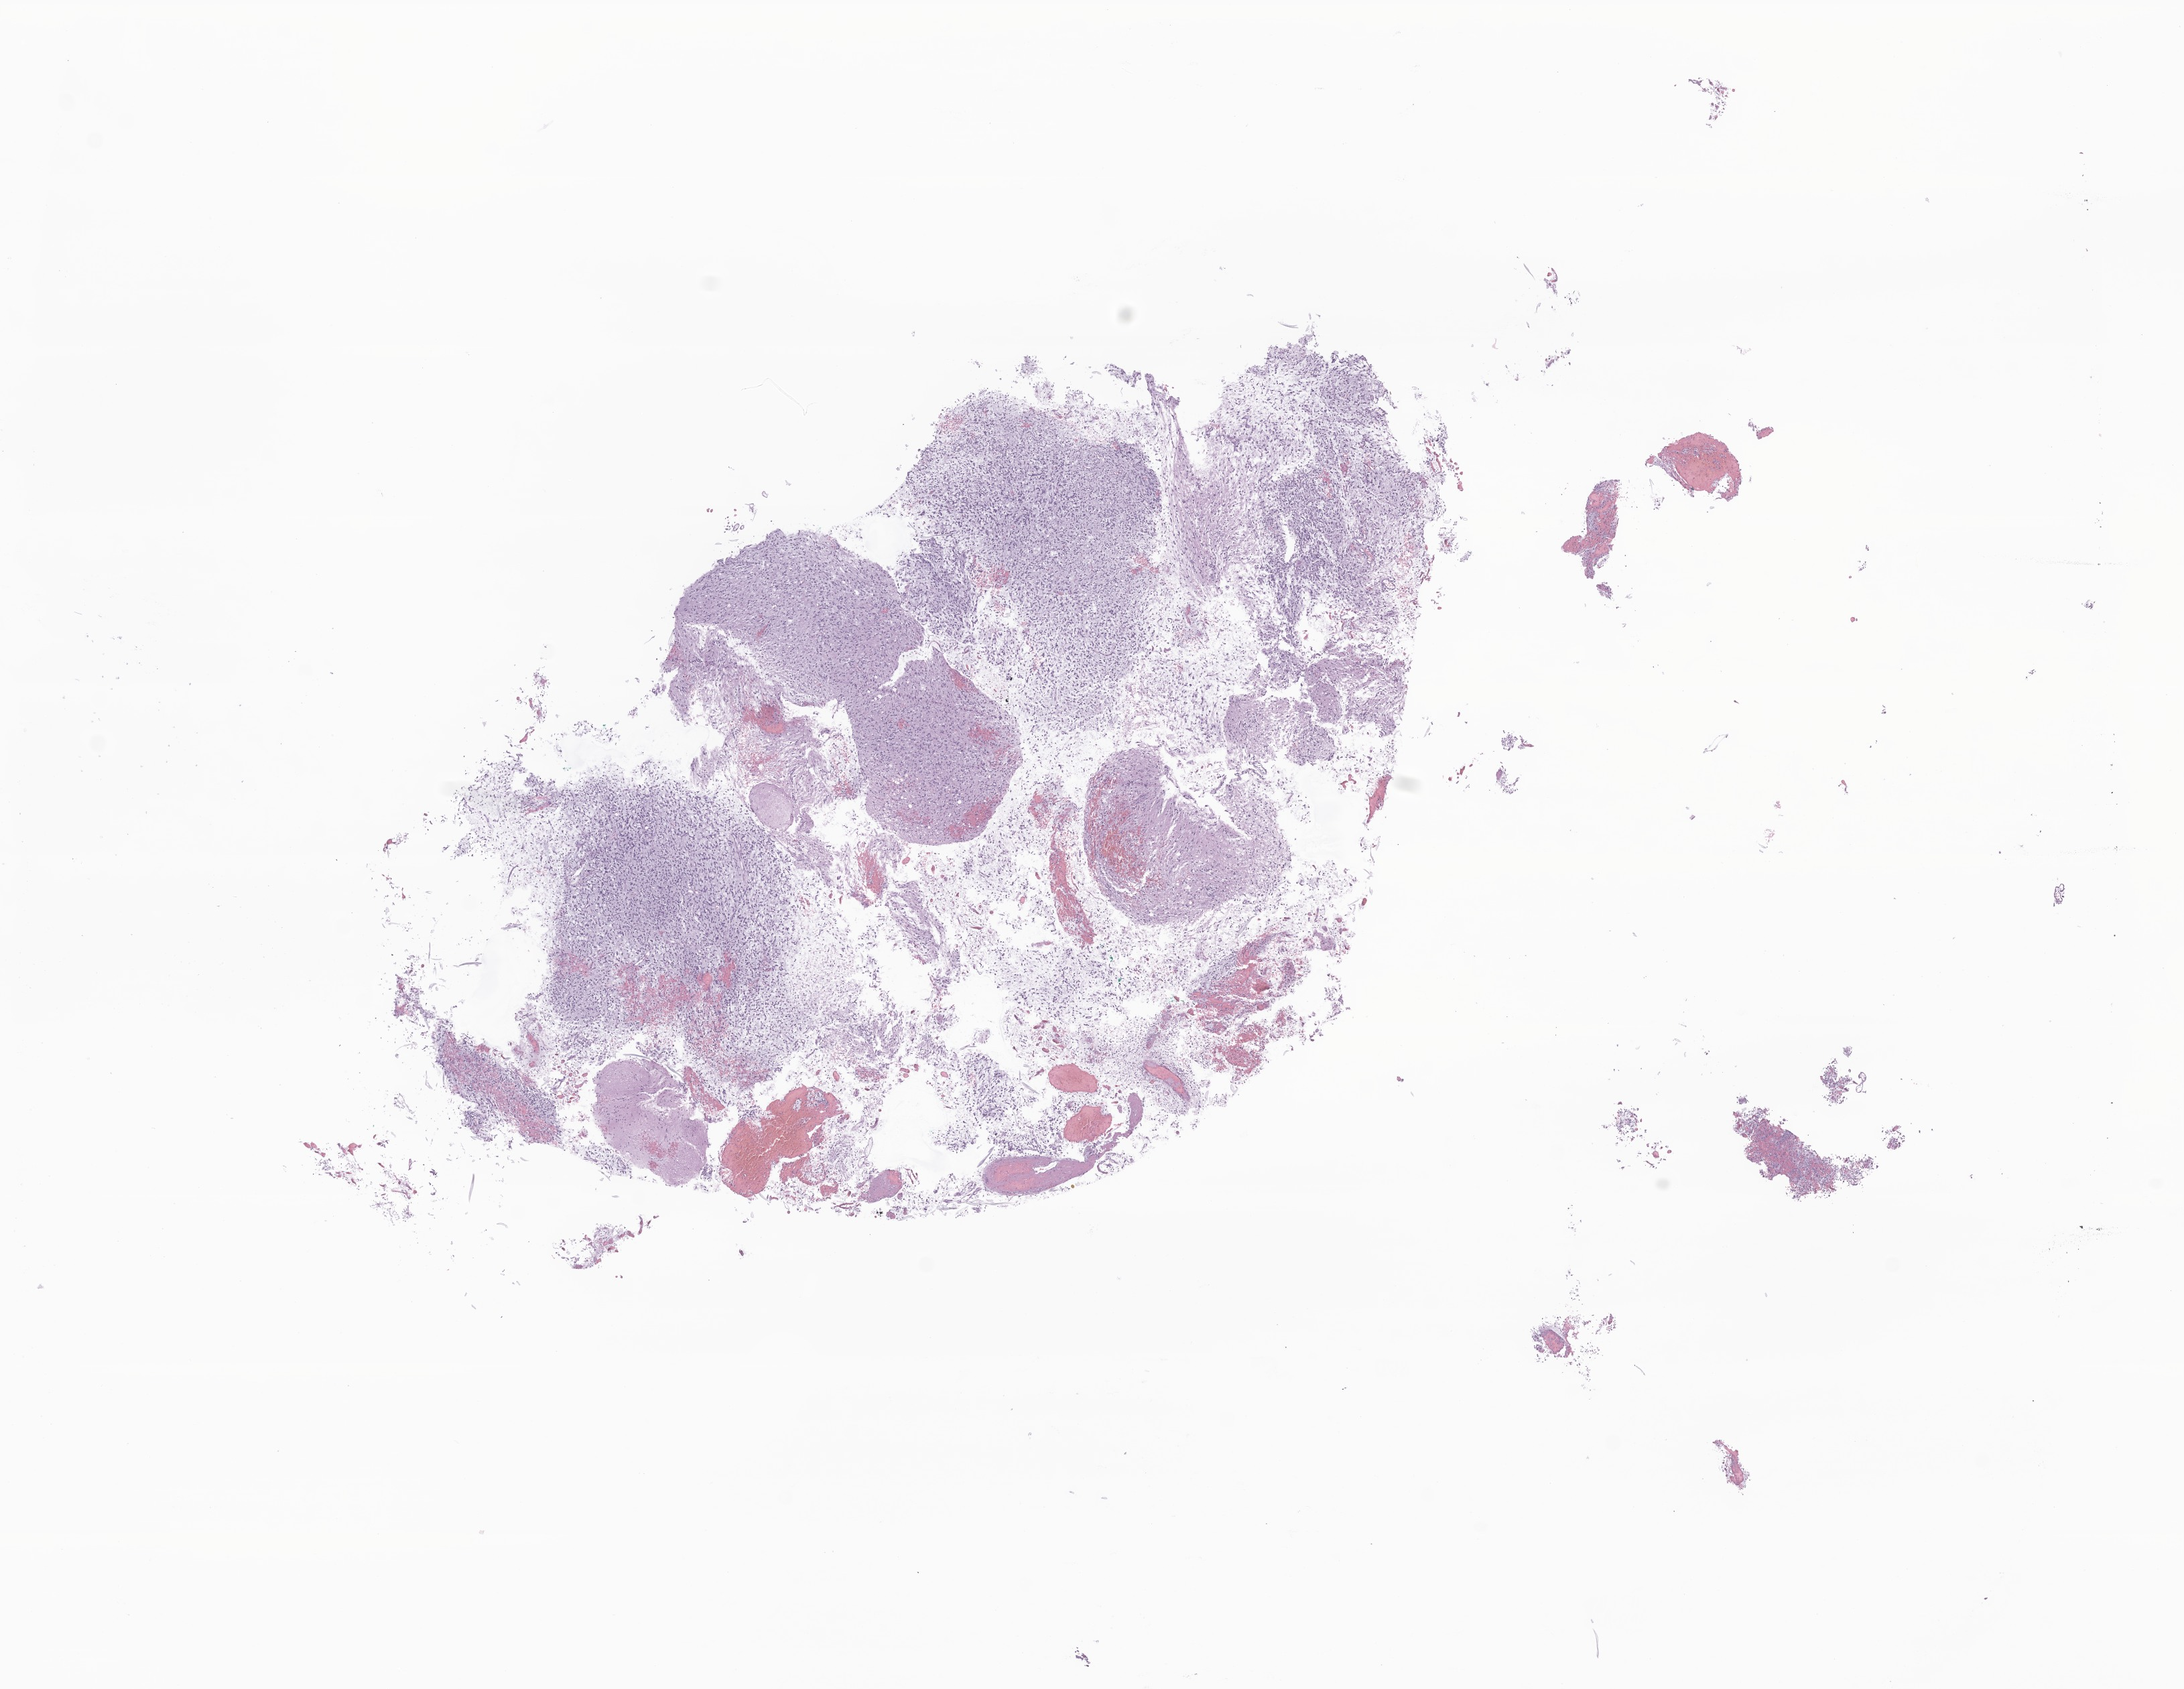
Digitized hematoxylin and eosin (H&E)-stained section of tumor tissue from the brain stem — shown as a low-resolution overview of the whole scanned area (about 13.7 x 10.6 mm). FFPE section. Male patient, age 107 months.
* diagnosis (ICD-O-3 morphology term): Glioma, malignant